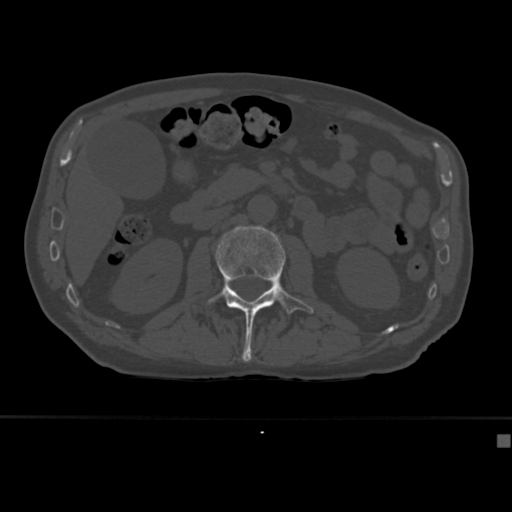
CT including the spine, one axial slice. Slice 148 of 430 in the series (ordered by position). 120 kVp. Bone window (W 1800 / L 400 HU). 512 × 512 image matrix, field of view 337 × 337 mm. Male patient, age 64 years. From the clinical record (not read from this slice): primary cancer: uterus; vertebrae with lytic lesions (as recorded): T1, T4, T5, T7, L5.
Structures marked on this image (semi-automatic segmentation, software-assisted and operator-edited):
- L2 vertebra: bounding box (x1, y1, x2, y2) in pixels: (207, 226, 314, 362)